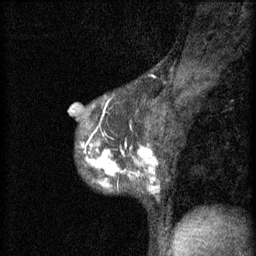
Breast MRI (dynamic contrast-enhanced), one sagittal slice. Position 38 of 60 along the scan axis. 3 images stored at this slice position (order not interpretable as contrast timing). 1.5 T. TE 4.2 ms, TR 11 ms. 2 mm slice thickness. 256 × 256 image matrix. Female patient, age 37 years.
Structures marked on this image (semi-automatically segmented with operator editing):
- analysis volume of interest (the breast-tissue region the enhancement analysis was run in; not a lesion): bounding box (x1, y1, x2, y2) in pixels: (78, 138, 160, 195)
- tumour enhancement mask (voxels above the 70 % enhancement threshold inside the analysis volume of interest): (81, 138, 159, 195)